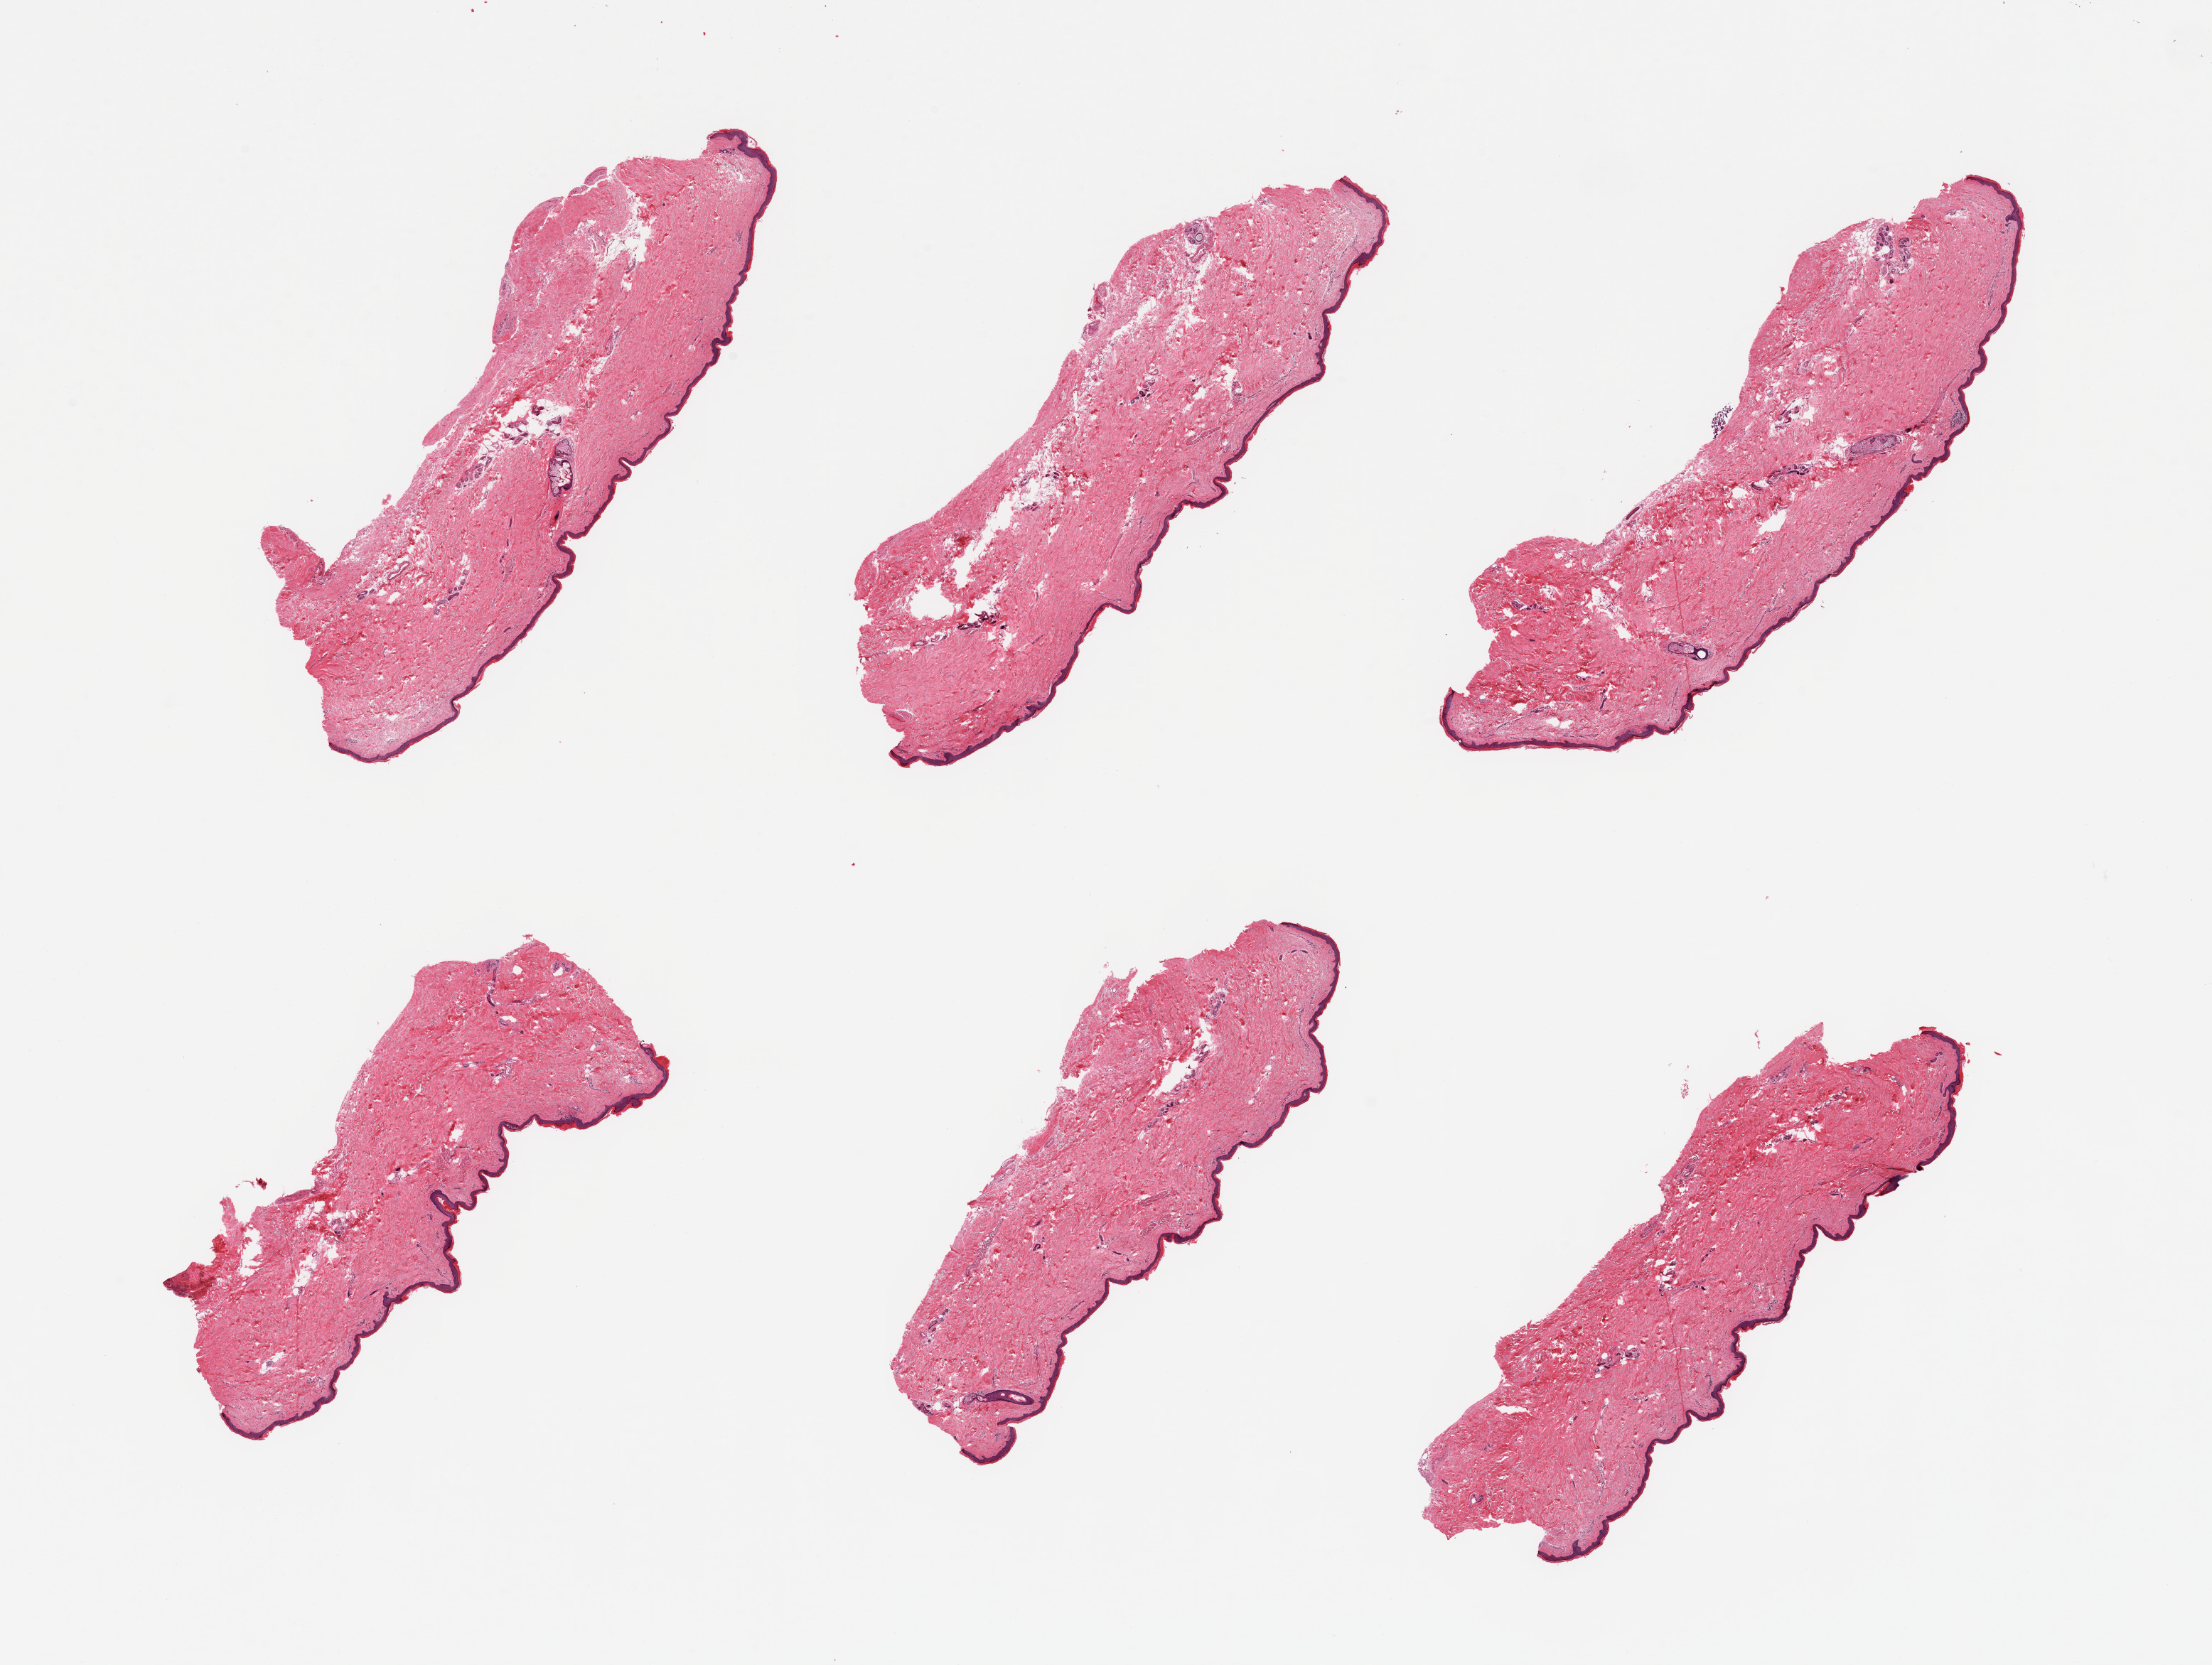
H&E whole-slide image, low-resolution overview of the scanned area, about 24.6 x 18.5 mm (from a 20x scan); PAXgene-fixed, paraffin-embedded tissue; sampled site (target tissue): skin of lower leg; tissue donor sample. Donor sex: male.
Reviewer comment on this tissue sample: 6 pieces, squamous epithelium is ~40-50 microns; no dermal fat.